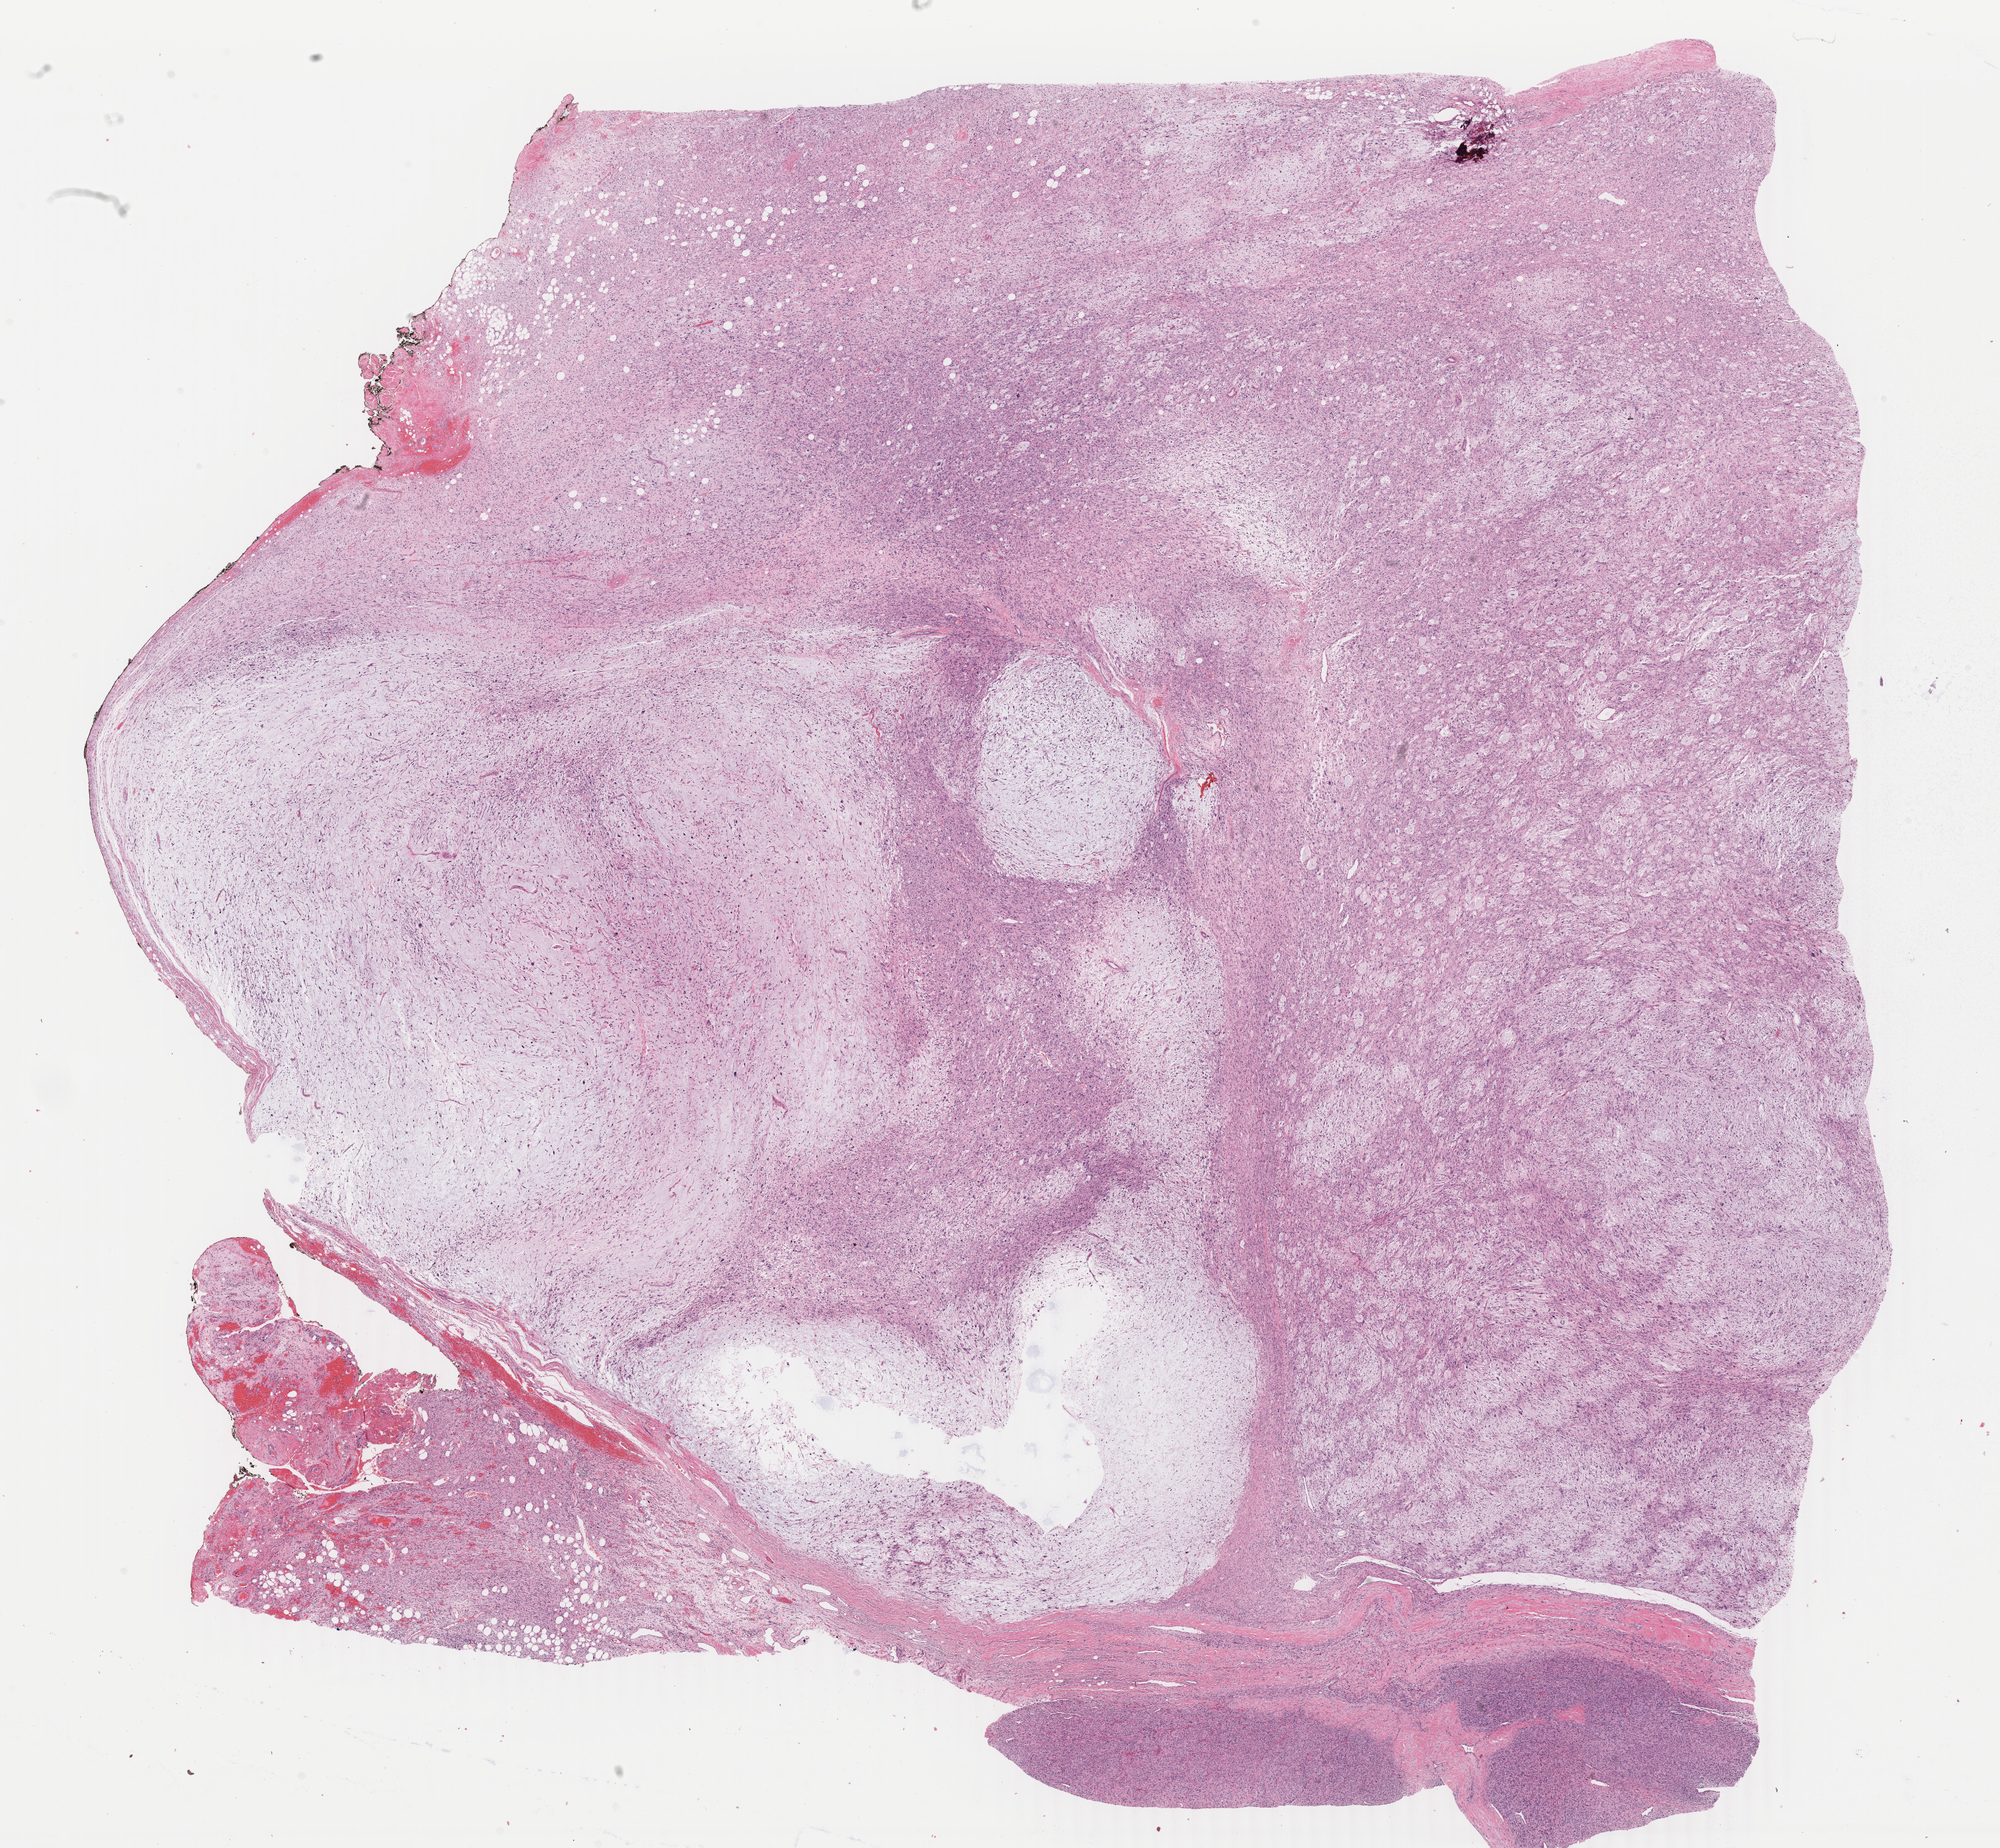
H&E-stained whole-slide image, low-resolution overview of the scanned area, about 24.0 x 22.2 mm (from a 40x scan); FFPE section; primary tumour sample from the connective, subcutaneous and other soft tissues. Patient: male, age at initial diagnosis 55 years.
Pathologic diagnosis: Fibromyxosarcoma (connective, subcutaneous and other soft tissues of lower limb and hip).